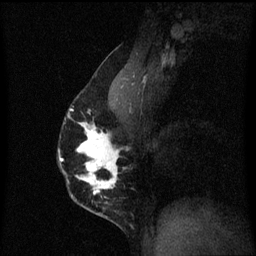
Breast MRI (dynamic contrast-enhanced), one sagittal slice. Position 38 of 60 along the scan axis. Dynamic contrast-enhanced series, image 2 of 3 at this slice position (ordered by acquisition). 1.5 T. TE 4.2 ms, TR 8.4 ms. 256 × 256 image matrix, field of view 200 × 200 mm. Female patient, age 40 years.
Outlined on this slice (semi-automatic segmentation, software-assisted and operator-edited):
- analysis volume of interest (the breast-tissue region the enhancement analysis was run in; not a lesion): bounding box (x1, y1, x2, y2) in pixels: (59, 88, 126, 211)
- tumour enhancement mask (voxels above the 70 % enhancement threshold inside the analysis volume of interest): (59, 110, 126, 197)